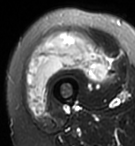
MRI of an extremity soft-tissue mass, one axial slice; T2-weighted fat-saturated; MR volume resampled by the dataset authors to the PET/CT grid (not the native acquisition matrix); 3.27 mm slice thickness; 135 × 146 image matrix, field of view 132 × 143 mm. Female patient. Case-level facts recorded for this patient, not image findings: histological type: pleiomorphic undifferentiated sarcoma; grade: high; site of the primary tumour: right quadricep.
Outlined on this slice (expert contour drawn on MRI and transferred to this co-registered scan by the dataset authors):
- gross tumour volume including surrounding oedema: bounding box <25,34,109,117> (left, top, right, bottom; pixels)
- gross tumour volume (mass): <25,34,109,117>